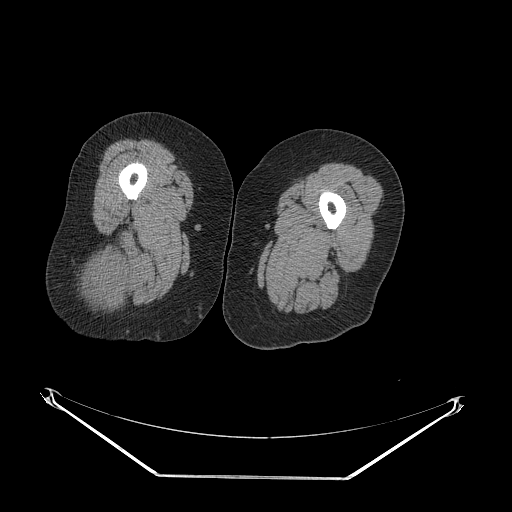
CT of an extremity soft-tissue mass (from a PET/CT study), one axial slice. Position 28 of 257 along the scan axis. 140 kVp. Soft-tissue window (W 400 / L 40 HU). 3.75 mm slice thickness. 512 × 512 image matrix. Female patient. From the clinical record (not read from this slice): histological type: synovial sarcoma; grade: intermediate; site of the primary tumour: right buttock.
Annotated regions visible in this slice (expert contour drawn on MRI and transferred to this co-registered scan by the dataset authors):
- gross tumour volume including surrounding oedema: box from (x=85, y=242) to (x=127, y=305) px
- gross tumour volume (mass): (x=85, y=254)–(x=127, y=303)